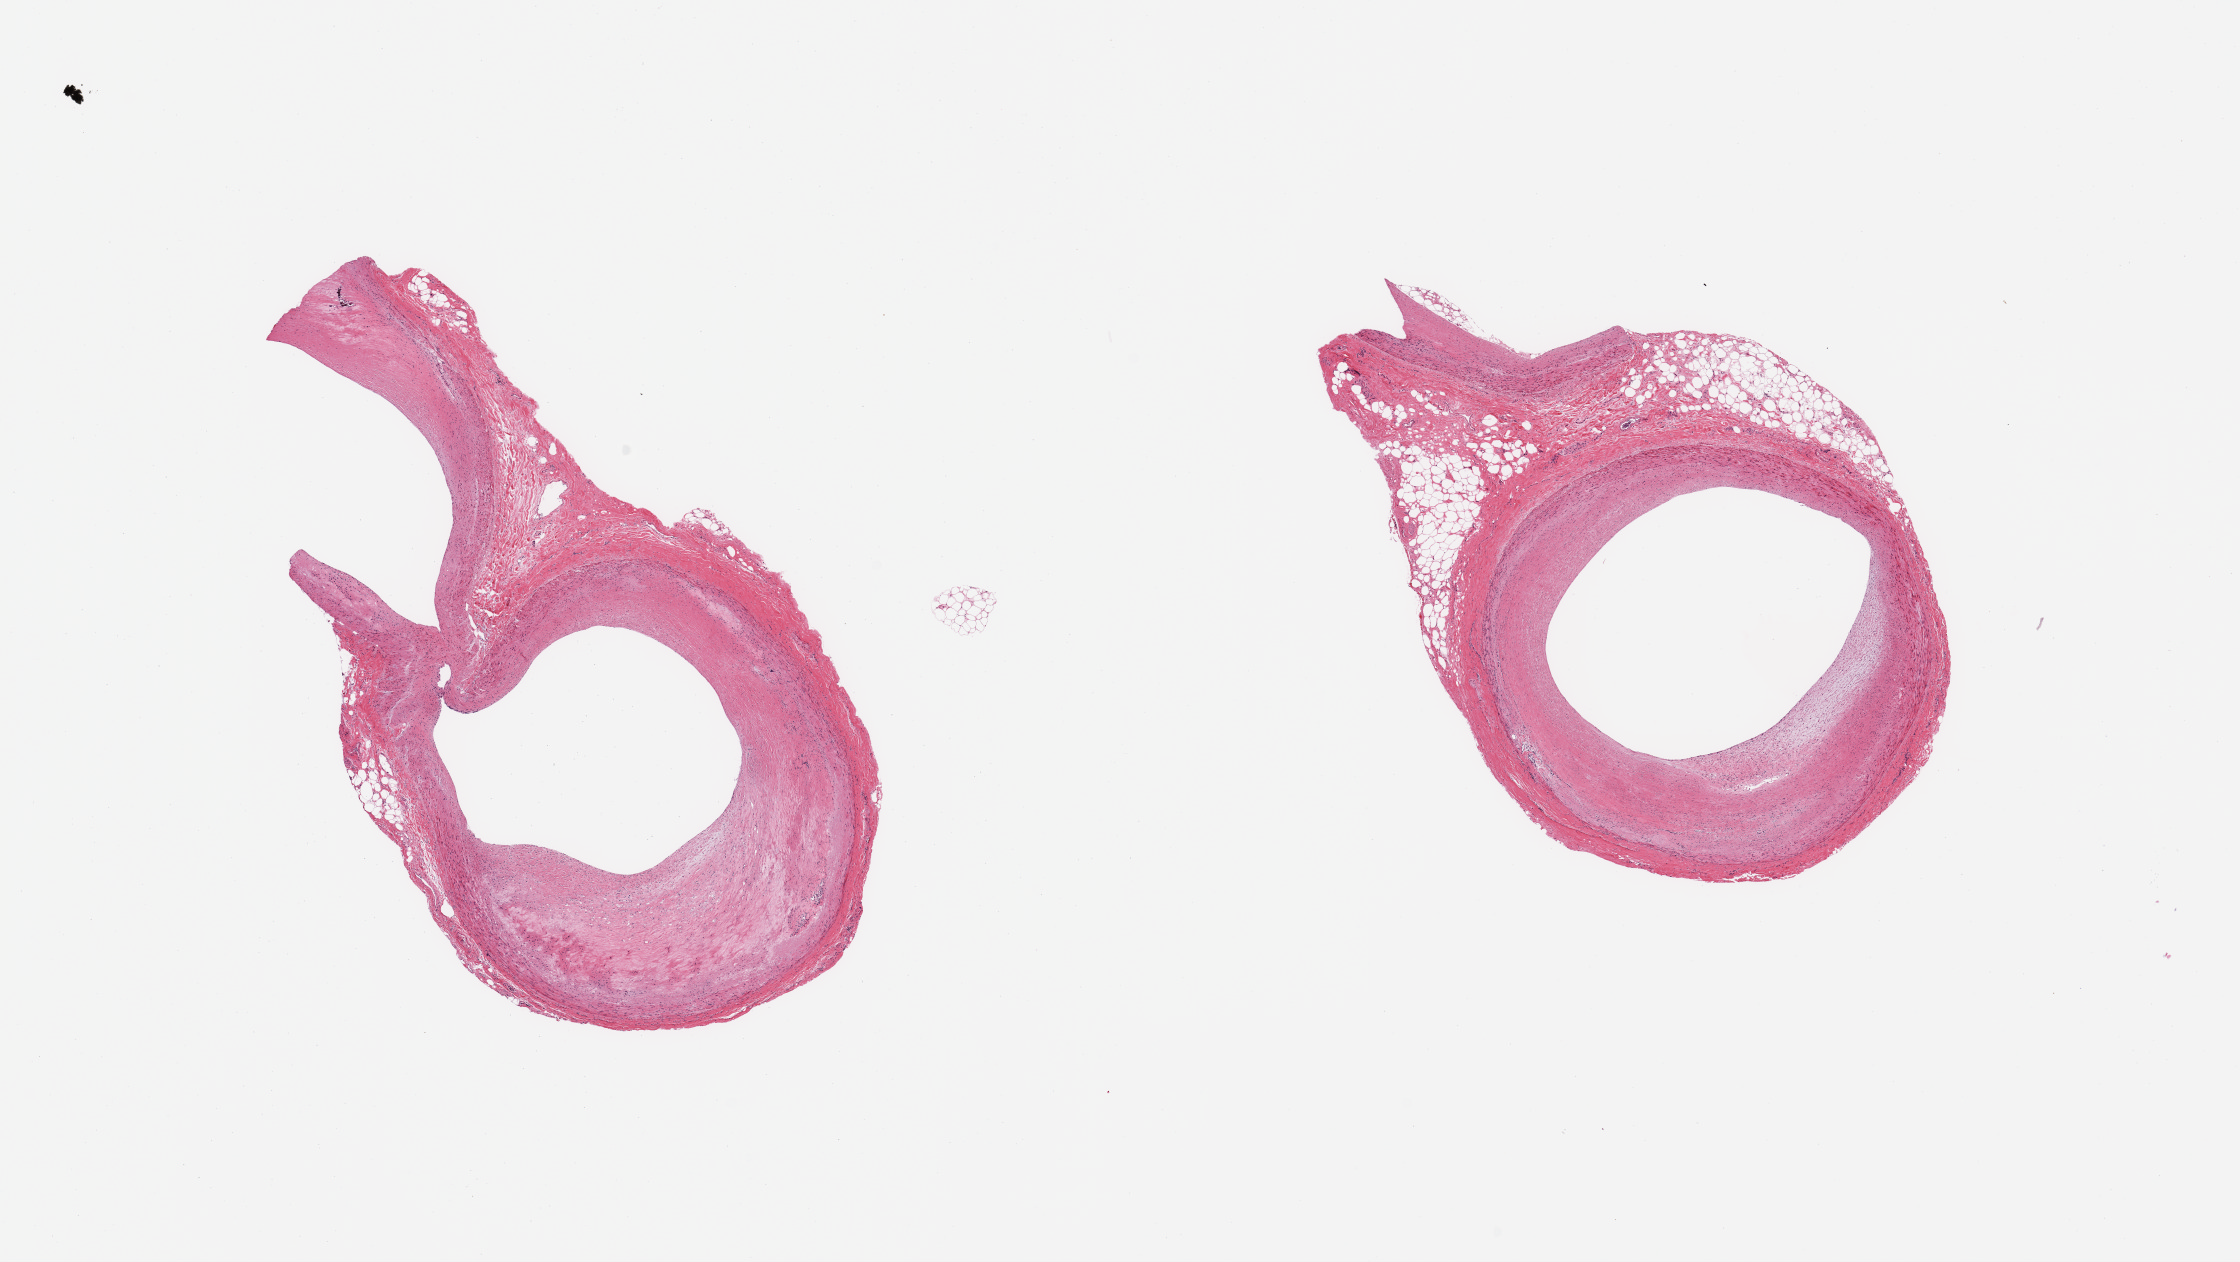
Whole-slide image, hematoxylin and eosin (H&E) stain, brightfield — whole scanned area (about 17.7 x 10.0 mm, from a 20x scan) shown as a low-resolution overview; PAXgene-fixed paraffin-embedded (PFPE) section; target tissue: coronary artery; tissue donor sample. Donor sex: male.
- reviewer comment on this tissue sample: 2 pieces, adherent fatty nubbin up to ~0.8mm; ~60-70% luminal occlusive atherosis